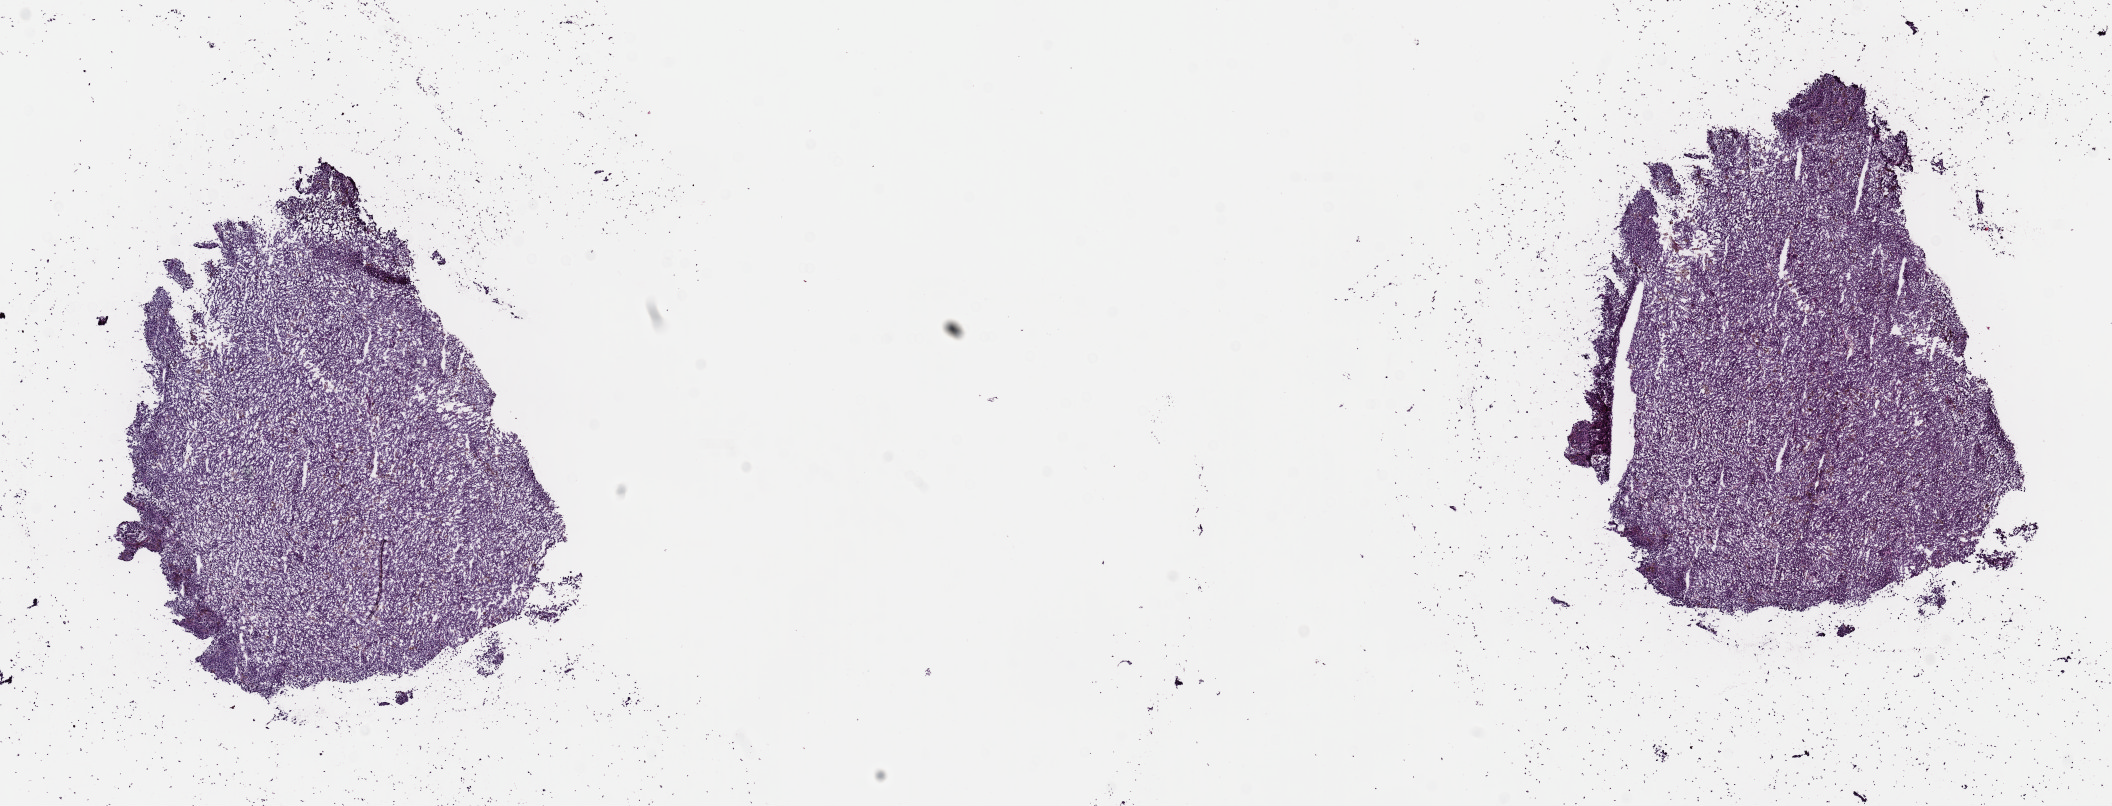
H&E whole-slide image, low-resolution overview of the scanned area, about 16.7 x 6.4 mm (from a 40x scan). Frozen section from the top of the tissue portion. Metastatic tumour sample, sampled site not recorded. Male patient; age at initial diagnosis 67 years. Pathologist review of this section (percent, as recorded): tumour cells 90%, tumour nuclei 90%, normal cells 0%, stromal cells 10%, necrosis 0%. Infiltration values recorded for this section: lymphocyte infiltration 2%, monocyte infiltration 1%, neutrophil infiltration 0%.
This section: metastatic tumour tissue. Patient diagnosis: Malignant melanoma, NOS.